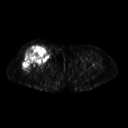
FDG PET of an extremity soft-tissue mass (from a PET/CT study), one axial slice; position 261 of 311 along the scan axis; 3.27 mm slice thickness; 128 × 128 image matrix. Patient: female, 57 years. From the clinical record (not read from this slice): histological type: pleiomorphic undifferentiated sarcoma; grade: high; site of the primary tumour: right quadricep.
Outlined on this slice (expert contour drawn on MRI and transferred to this co-registered scan by the dataset authors):
- tumour plus oedema (research contour): bounding box [x1, y1, x2, y2] px = [22, 46, 49, 71]
- tumour (research contour): [22, 46, 49, 71]